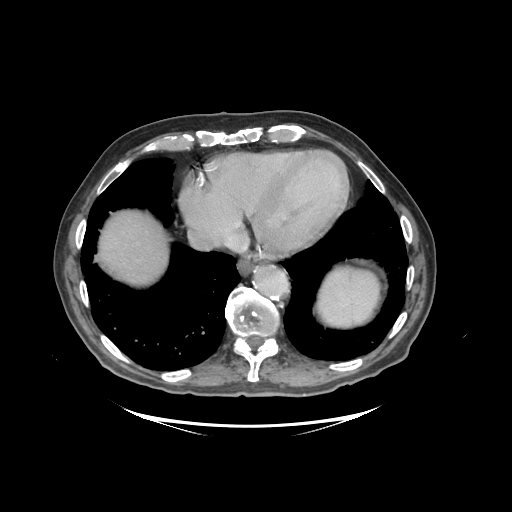
Contrast-enhanced abdominal CT (liver protocol), one axial slice. Slice 89 of 99 in the series (ordered by position). Reconstruction kernel STANDARD. 140 kVp. Soft-tissue window (W 400 / L 40 HU). 512 × 512 image matrix, field of view 460 × 460 mm. From the clinical record (not read from this slice): diagnosis: hepatocellular carcinoma (patient treated with transarterial chemoembolisation; whether this scan precedes or follows treatment is not stated here); TNM stage (as recorded): Stage-I; Child-Pugh class: A.
Structures marked on this image (semi-automatically segmented with operator editing):
- abdominal aorta: box from (x=256, y=266) to (x=287, y=296) px
- liver parenchyma outside the tumour (the mass and vessels are separate outlines, so this box may not span the whole liver): (x=98, y=210)–(x=168, y=284)